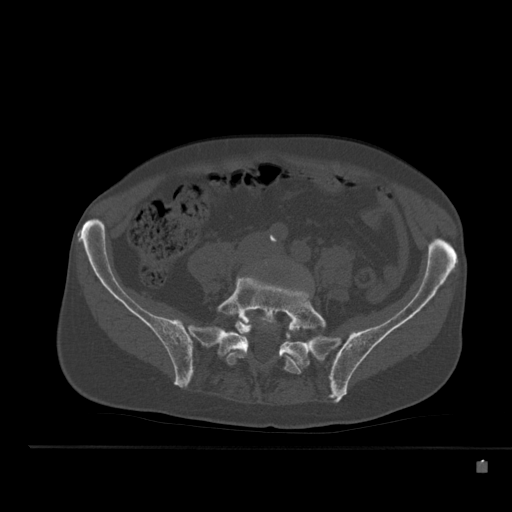
CT including the spine, one axial slice. Slice 122 of 517 in the series (ordered by position). 120 kVp. Bone window (W 1800 / L 400 HU). 1.5 mm slice thickness. 512 × 512 image matrix, field of view 408 × 408 mm. Patient: male, 70 years. From the clinical record (not read from this slice): primary cancer: renal.
Annotated regions visible in this slice (semi-automatic segmentation, software-assisted and operator-edited):
- L5 vertebra: bounding box <216,277,327,386> (left, top, right, bottom; pixels)